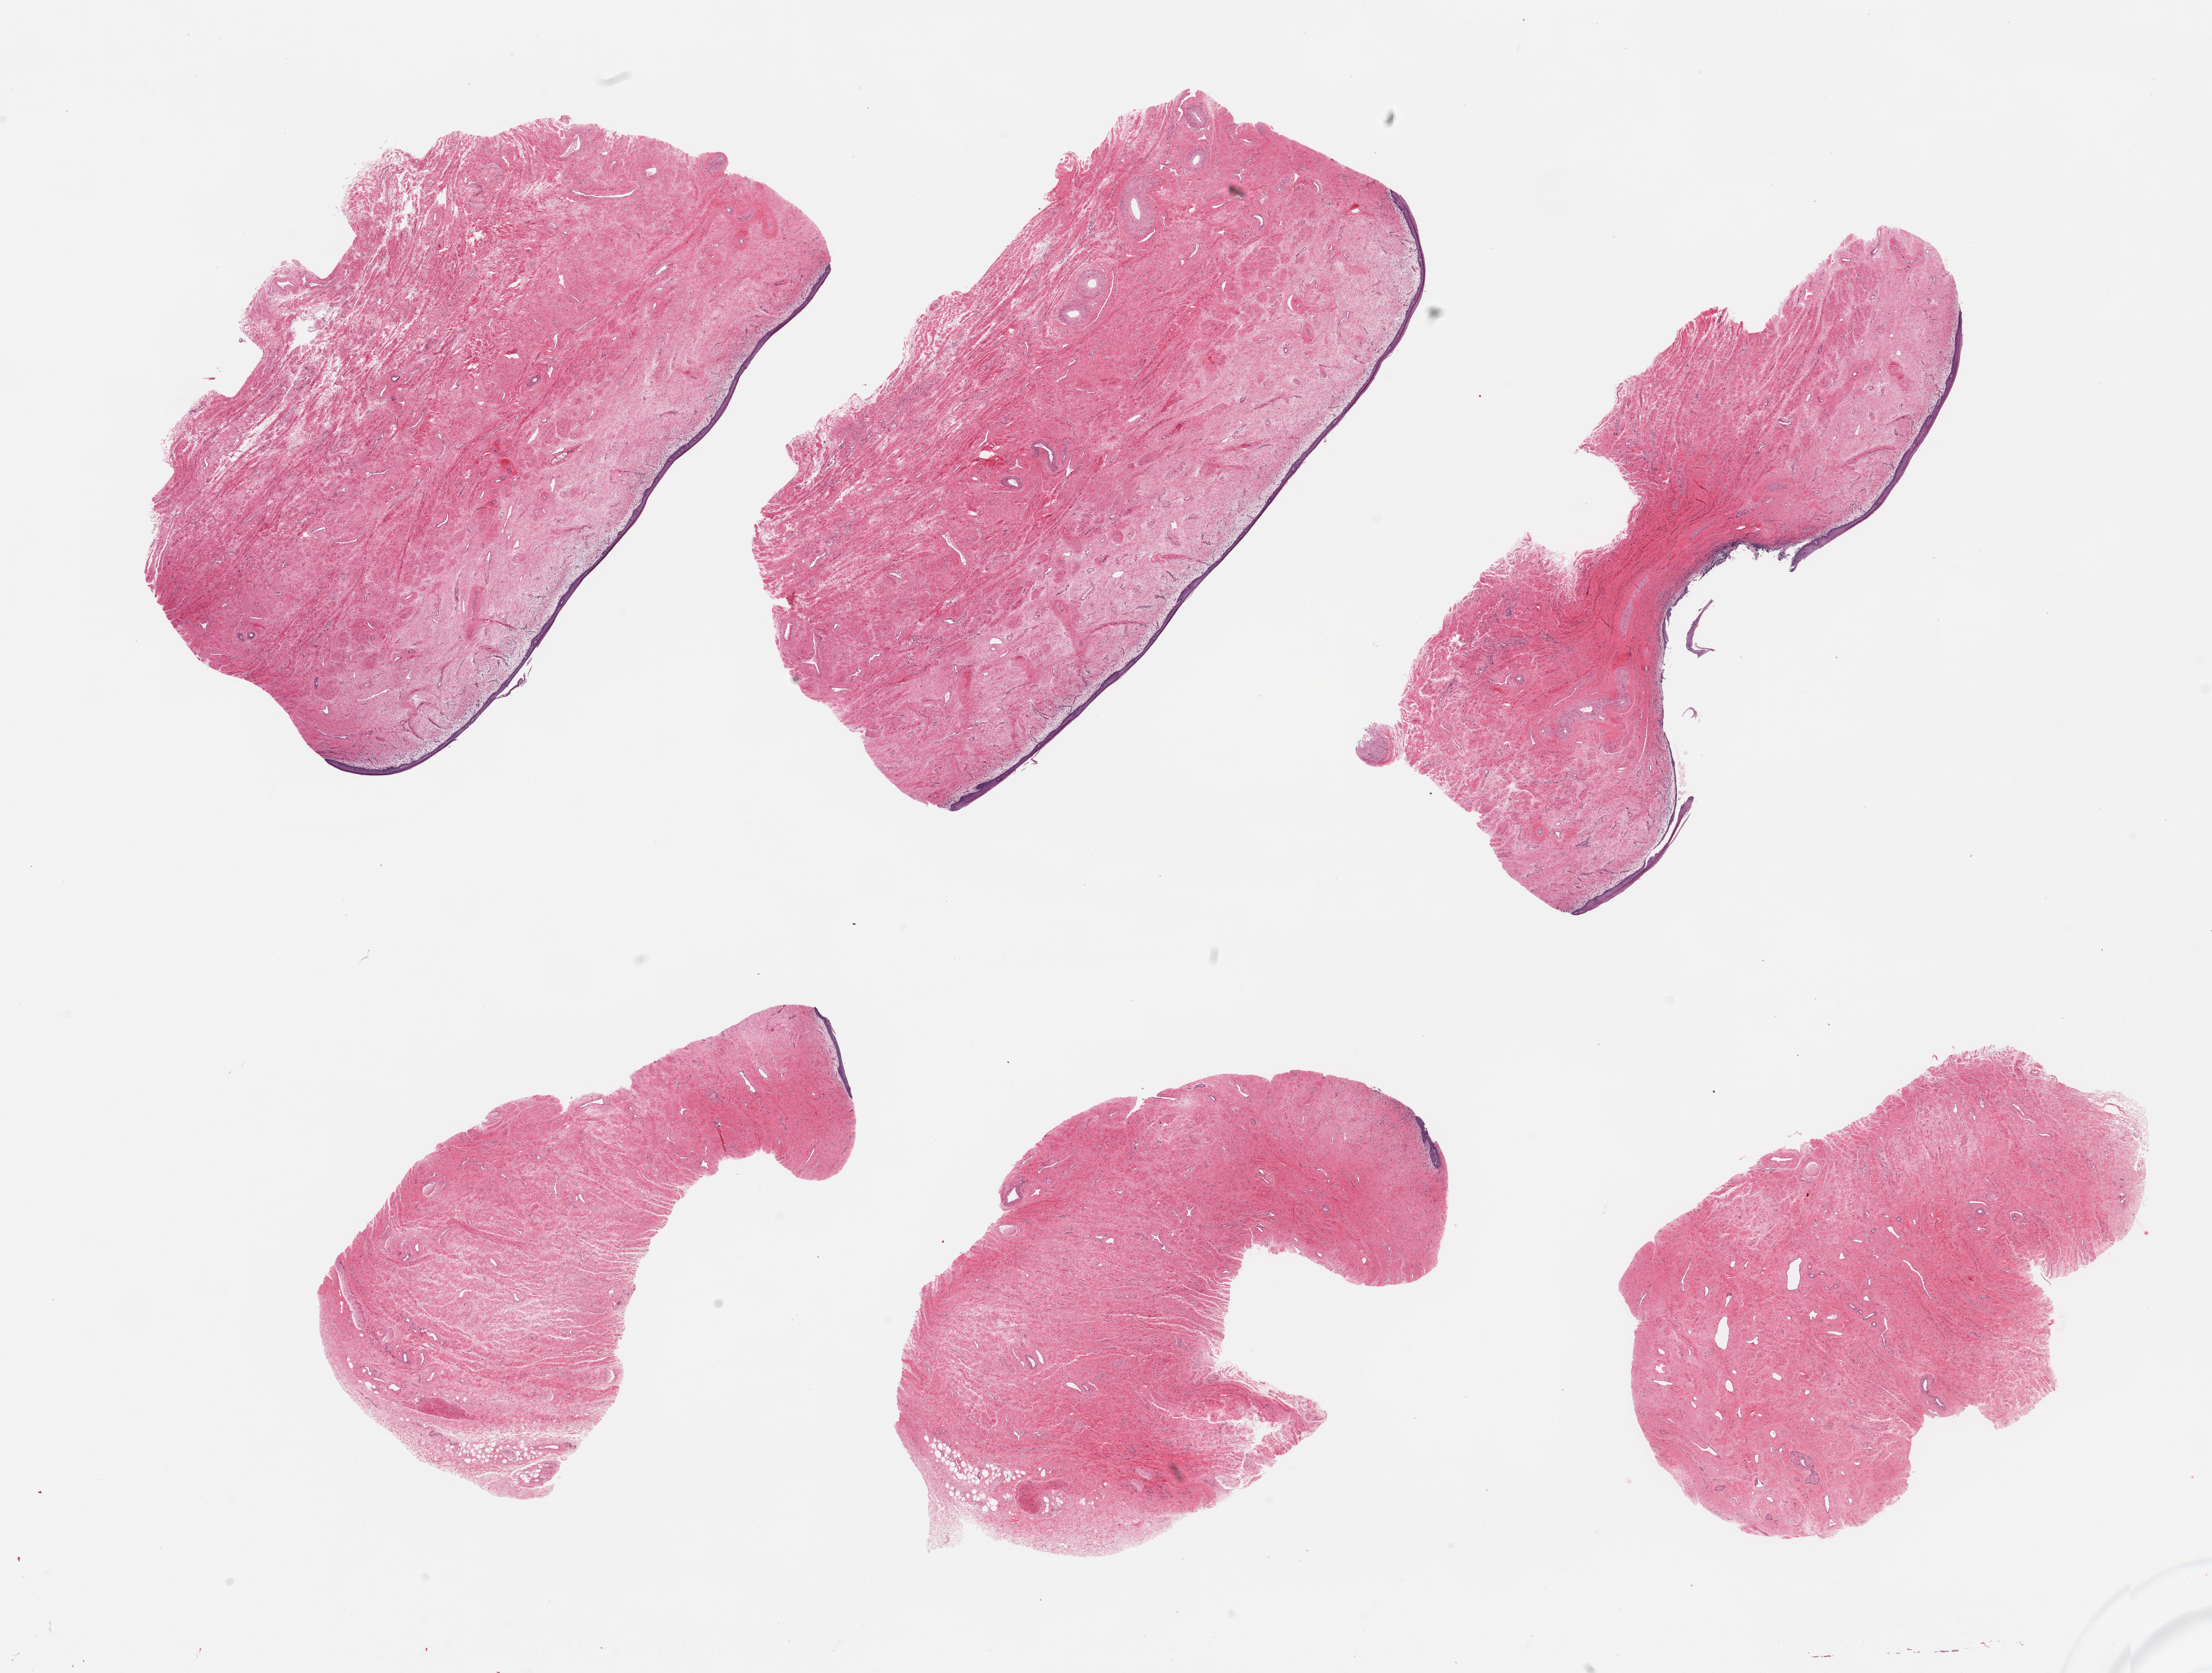
Digitized hematoxylin and eosin (H&E)-stained section, a low-resolution overview of the entire scanned area, about 26.6 x 20.1 mm (acquisition: 20x scan); PAXgene-fixed, paraffin-embedded tissue; sampled site (target tissue): vagina; donor tissue sample. Donor: female.
Review note (as recorded): 6 pieces, atrophic squamous mucosa.